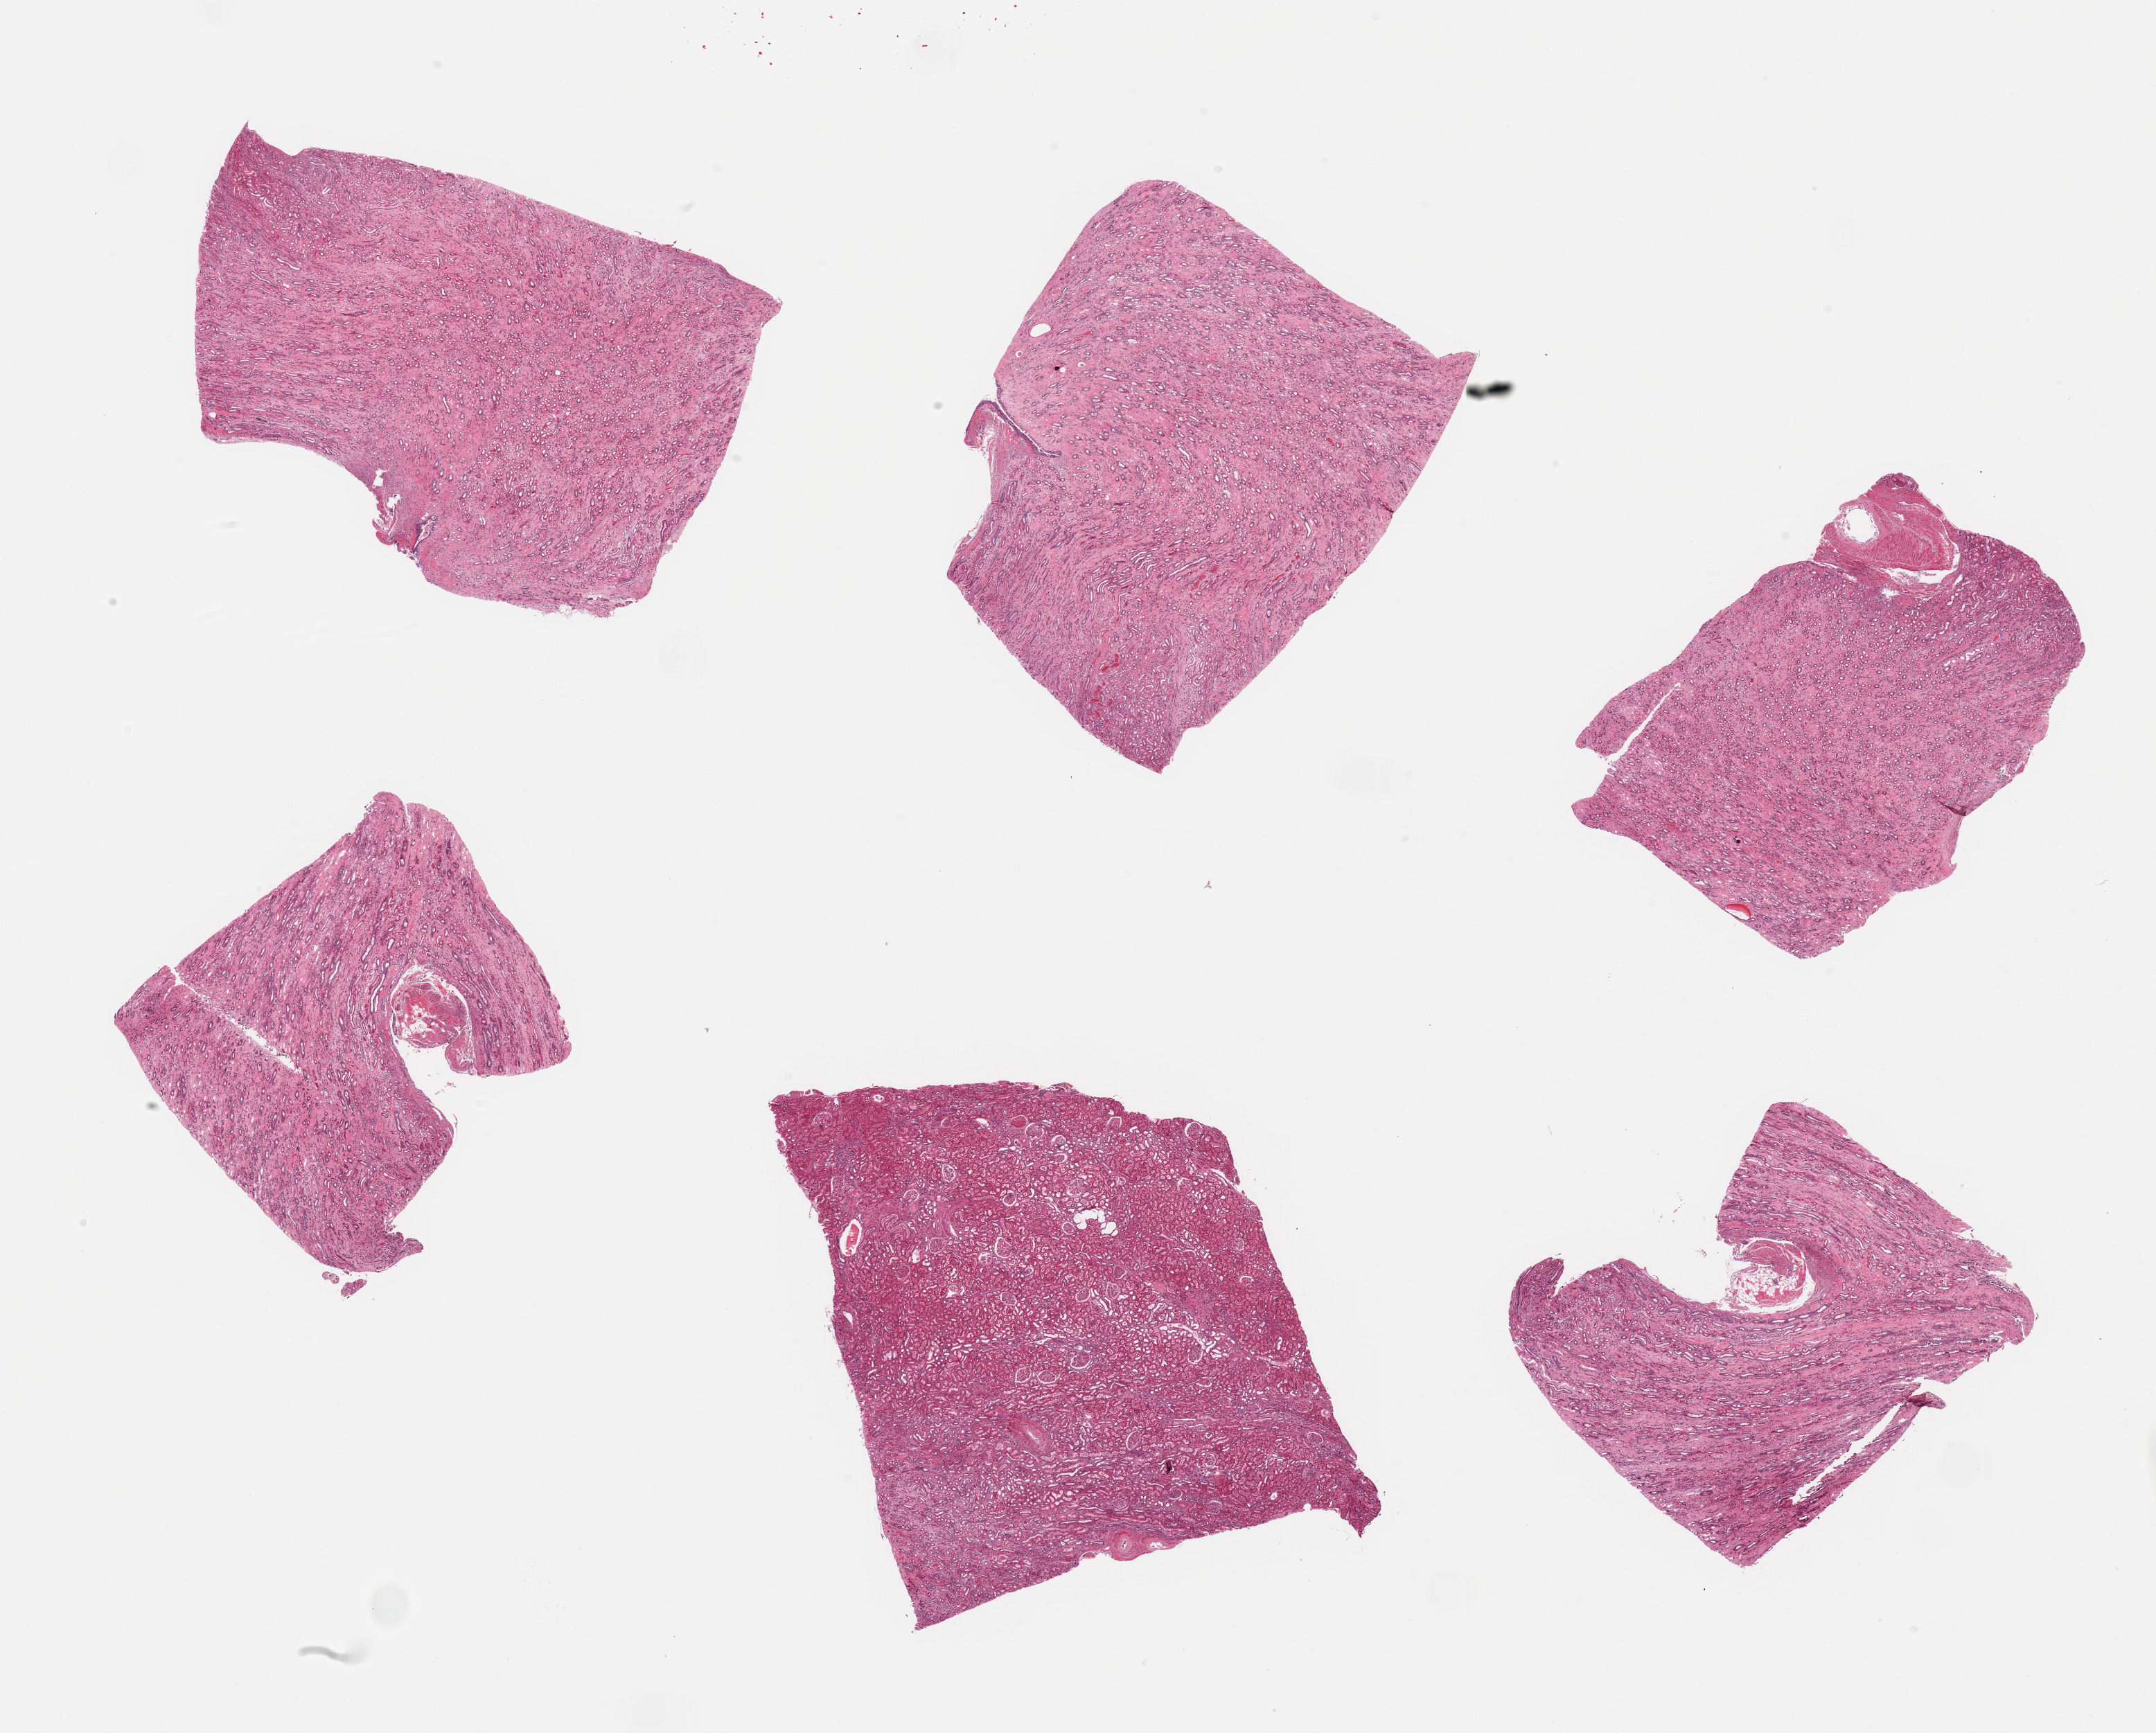
Digitized haematoxylin and eosin-stained section, a low-resolution overview of the entire scanned area, about 24.6 x 19.8 mm; PAXgene-fixed paraffin-embedded (PFPE) section; sampled site (target tissue): renal cortex; donor tissue sample. Donor sex: female.
- reviewer comment on this tissue sample: 6 pieces; only 1 of 6 contains cortex; others are medulla